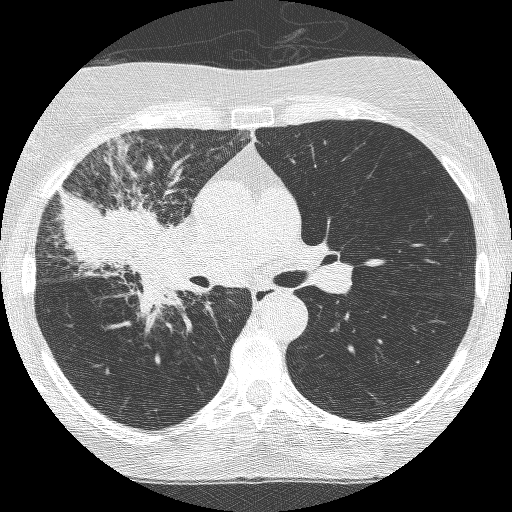
Low-dose screening chest CT, axial slice; third screening round (two years after baseline); lung window (W 1500 / L -600 HU); slice 153 of 253 in the series; 512 × 512 image matrix, field of view 294 × 294 mm. Female, age 64 years at enrolment. Former smoker at enrolment.
Expert reader's lesion annotation, box from (x=72, y=190) to (x=202, y=322) px. Screening reader's record for this exam (one nodule recorded; not confirmed to be the boxed lesion): non-calcified nodule or mass ≥4 mm, right upper lobe, 49 × 43 mm, spiculated (stellate) margins, soft tissue attenuation, pre-existing on the prior screen: yes; interval growth: yes.